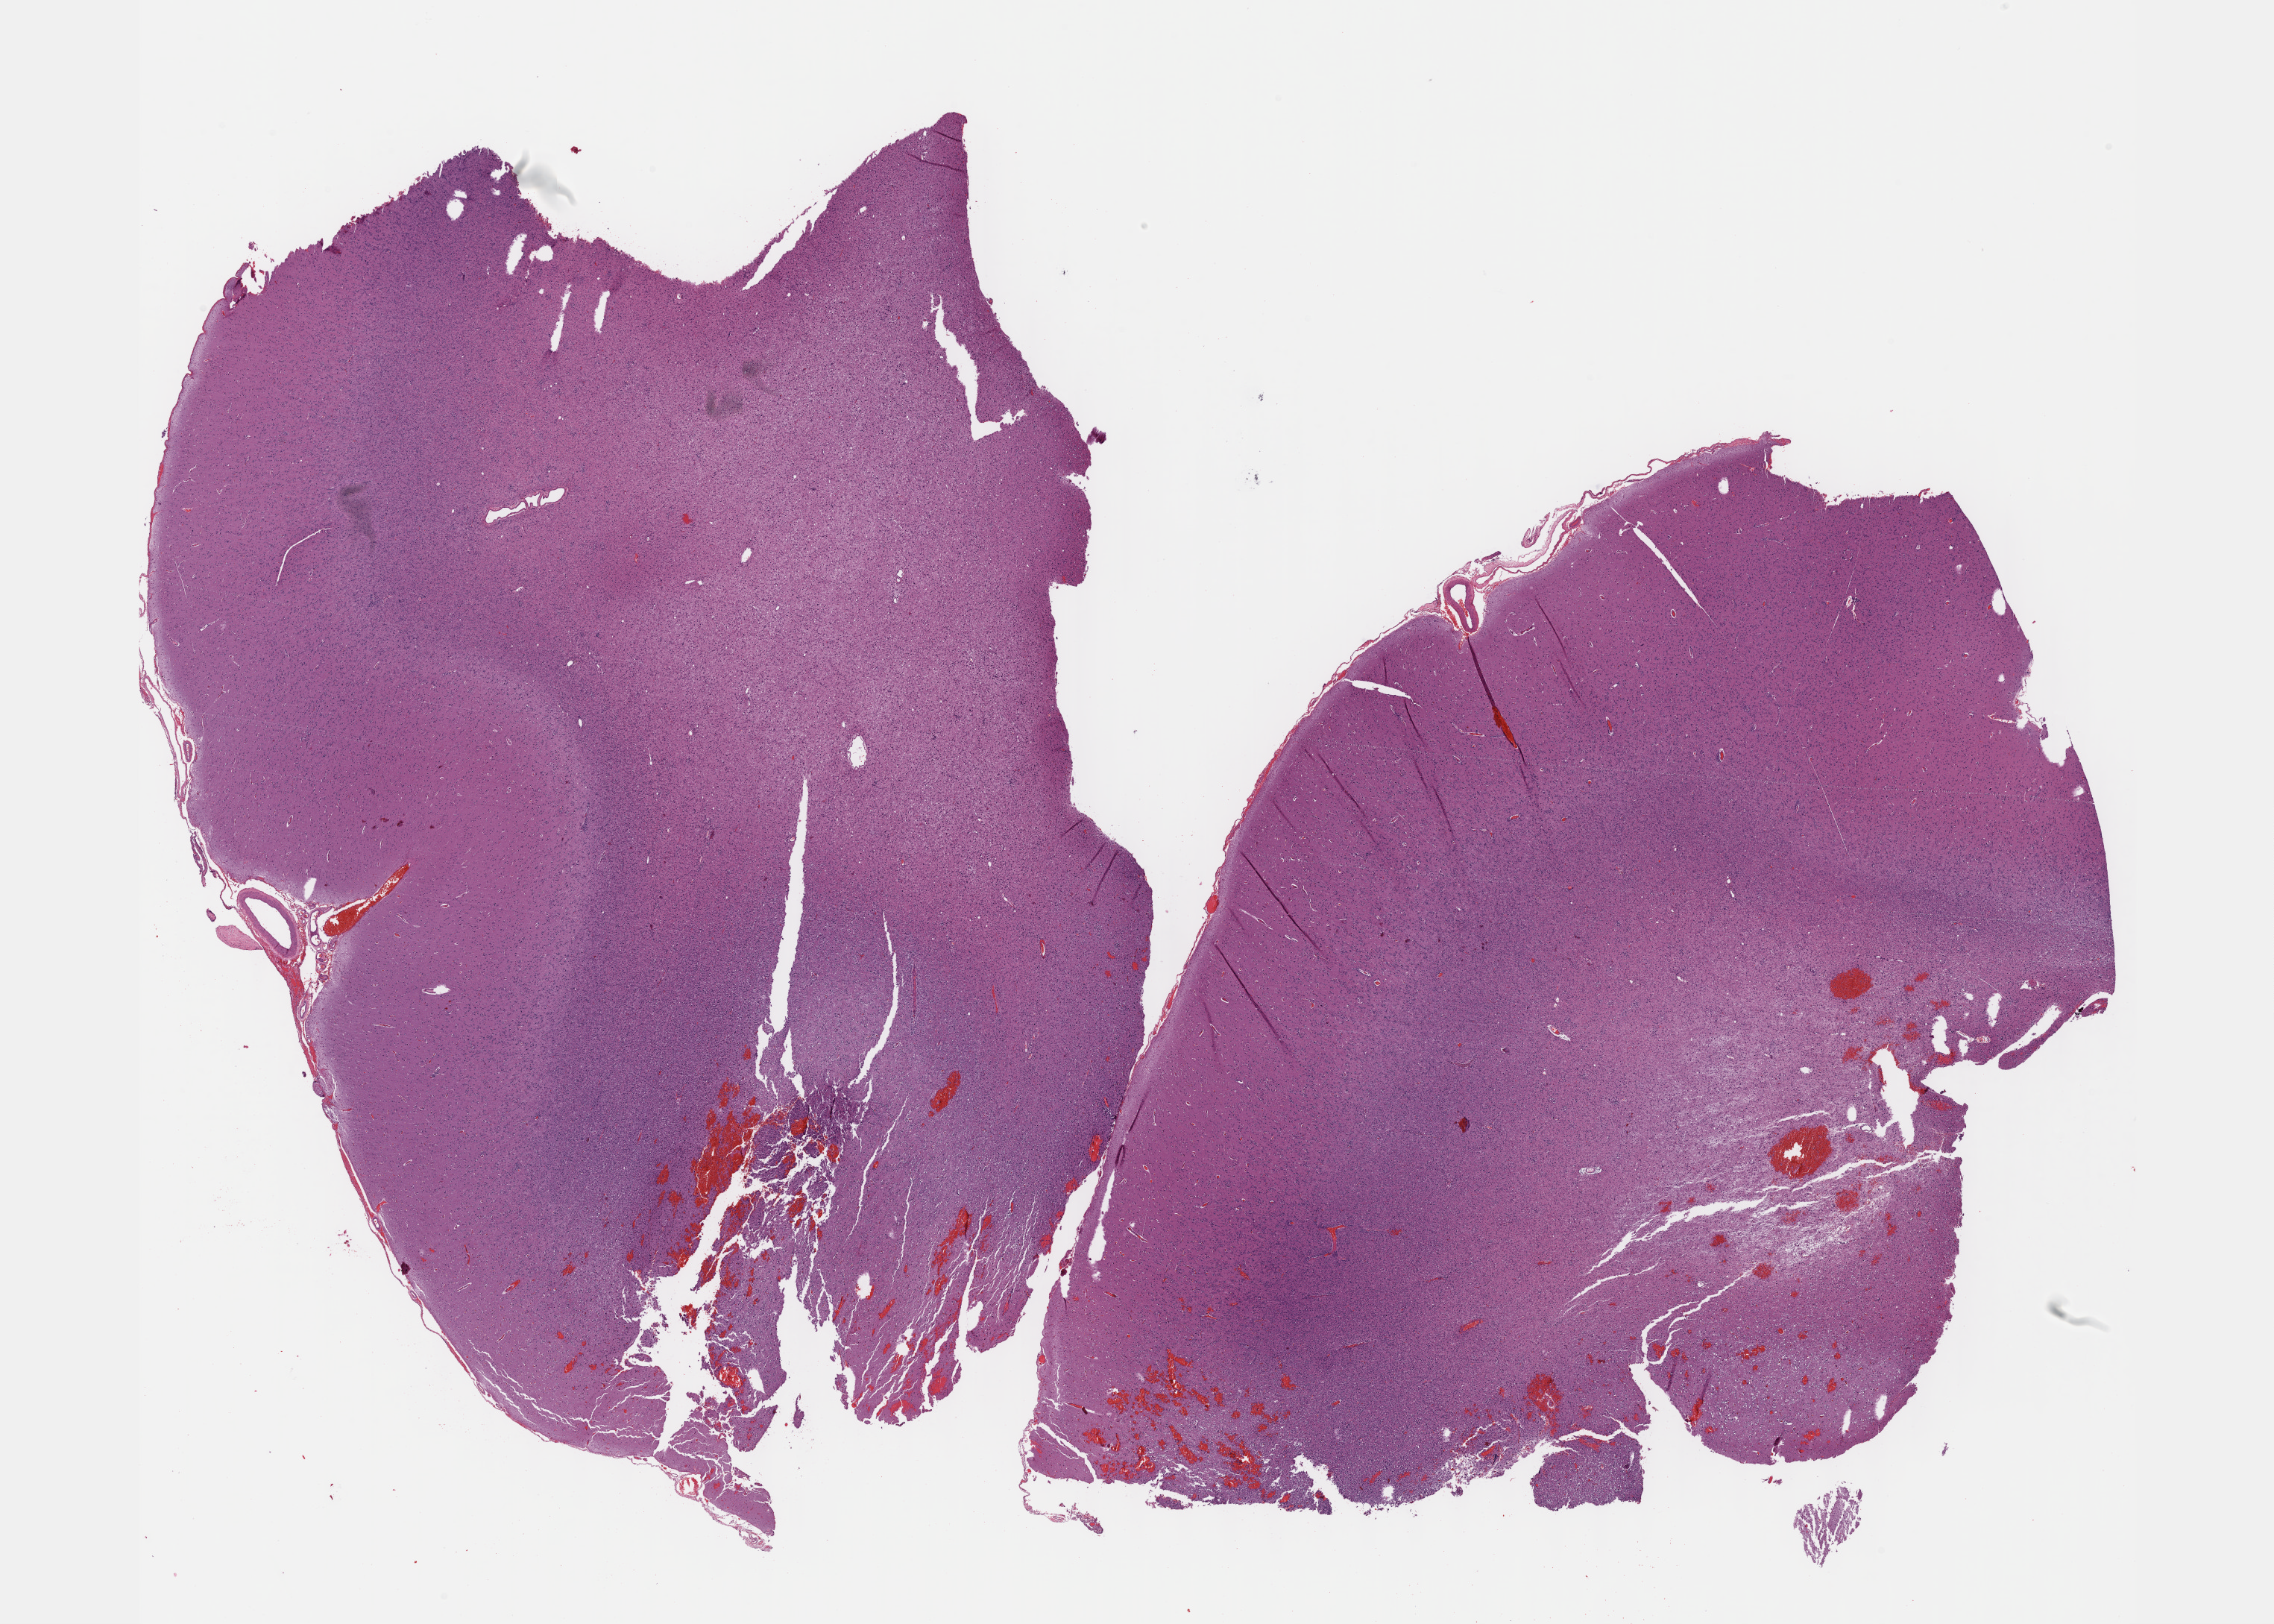
Digitized H&E tissue section (whole slide) — a low-resolution overview of the entire scanned area, about 24.6 x 17.6 mm, FFPE section, sample: primary tumour, brain. Male patient; age at initial diagnosis 59 years. Histologic grade: G3 (poorly differentiated).
Laterality: left. Pathologic diagnosis: Oligodendroglioma, anaplastic (cerebrum).